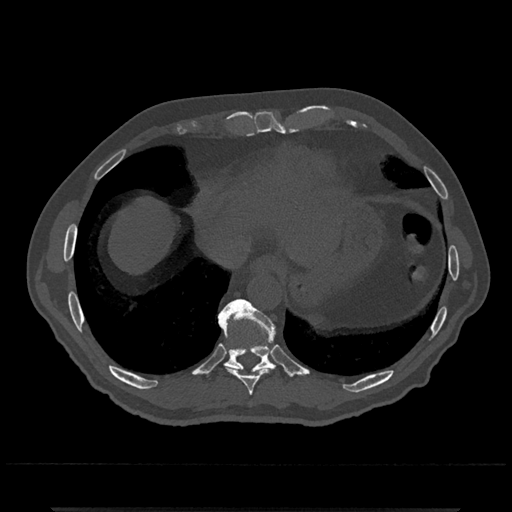
CT including the spine, one axial slice; slice 585 of 797 in the series (ordered by position); reconstruction kernel Br40s/3; bone window (W 1800 / L 400 HU); 512 × 512 image matrix. Patient: male, 67 years. Case-level facts recorded for this patient, not image findings: primary cancer: prostate.
Structures marked on this image (semi-automatic segmentation, software-assisted and operator-edited):
- T10 vertebra: bounding box (x1, y1, x2, y2) in pixels: (219, 299, 276, 373)
- T9 vertebra: (226, 367, 268, 396)